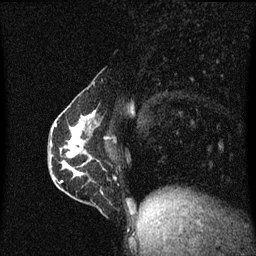
Breast MRI (dynamic contrast-enhanced), one sagittal slice; position 23 of 60 along the scan axis; dynamic contrast-enhanced series, image 2 of 3 at this slice position (ordered by acquisition); 1.5 T; TE 4.2 ms, TR 8.4 ms; 2 mm slice thickness; 256 × 256 image matrix. Patient: female, 40 years.
Annotated regions visible in this slice (semi-automatic segmentation, software-assisted and operator-edited):
- analysis volume of interest (the breast-tissue region the enhancement analysis was run in; not a lesion): bounding box [x1, y1, x2, y2] px = [57, 110, 108, 191]
- tumour enhancement mask (voxels above the 70 % enhancement threshold inside the analysis volume of interest): [60, 112, 95, 183]